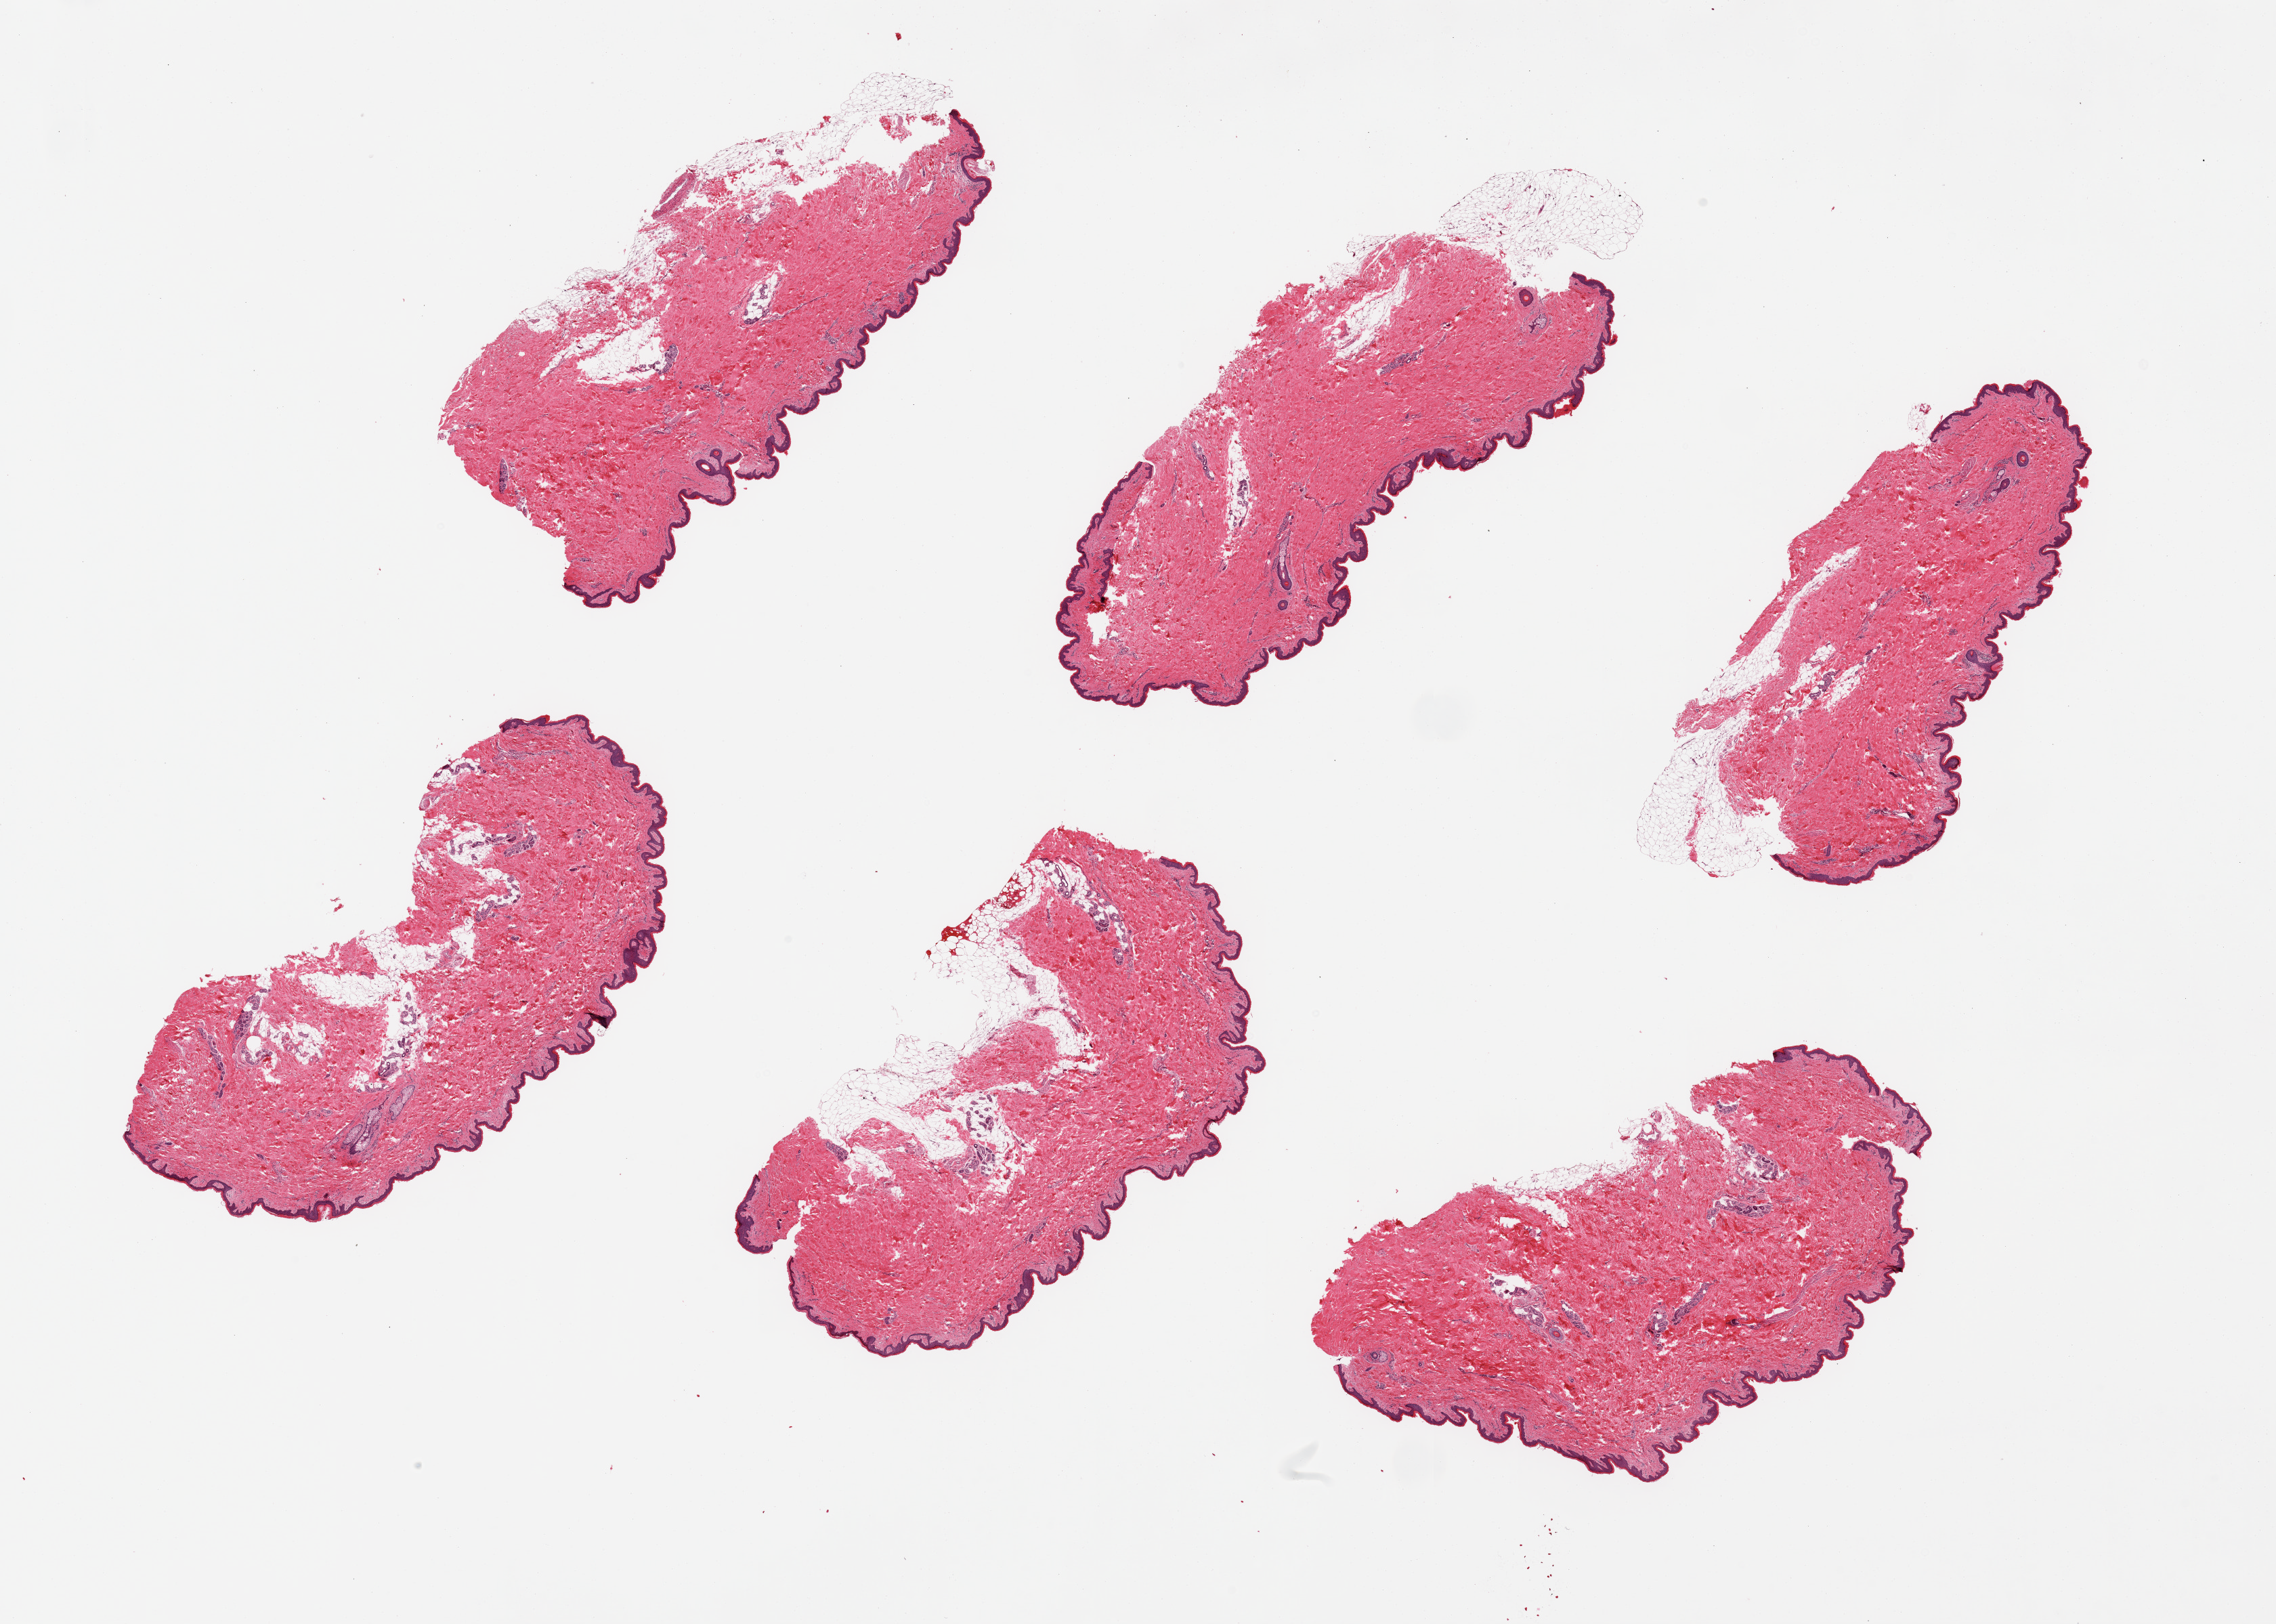
Haematoxylin and eosin whole-slide image — a low-resolution overview of the entire scanned area, about 26.6 x 19.0 mm (acquisition: 20x scan), PAXgene-fixed, paraffin-embedded tissue, sampled site (target tissue): skin of suprapubic region, tissue donor sample.
* pathologist's review note for this sample: 6 pieces; 10% dermal fat